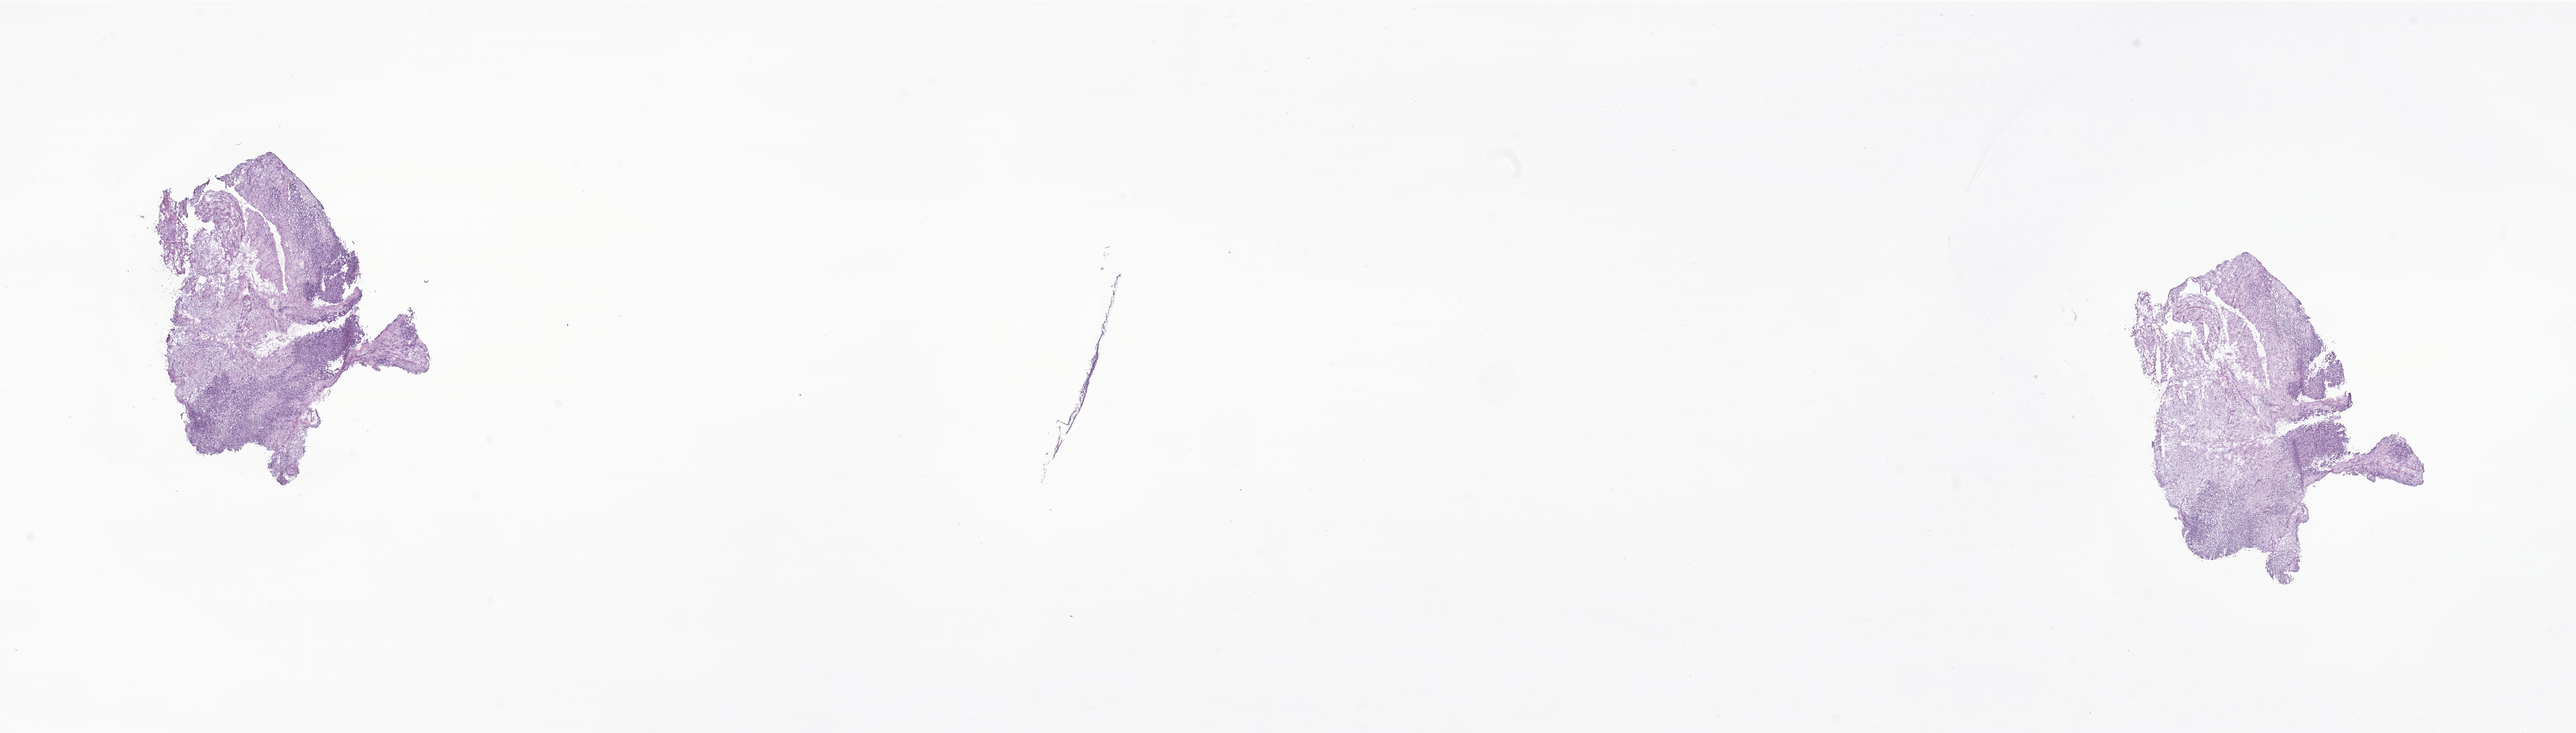
H&E whole-slide image of tumor tissue from the oropharynx — shown as a low-resolution overview of the whole scanned area (about 31.7 x 9.0 mm), frozen section. Female patient, age 71 months (5 years 11 months).
Recorded diagnosis: Mixed type rhabdomyosarcoma.